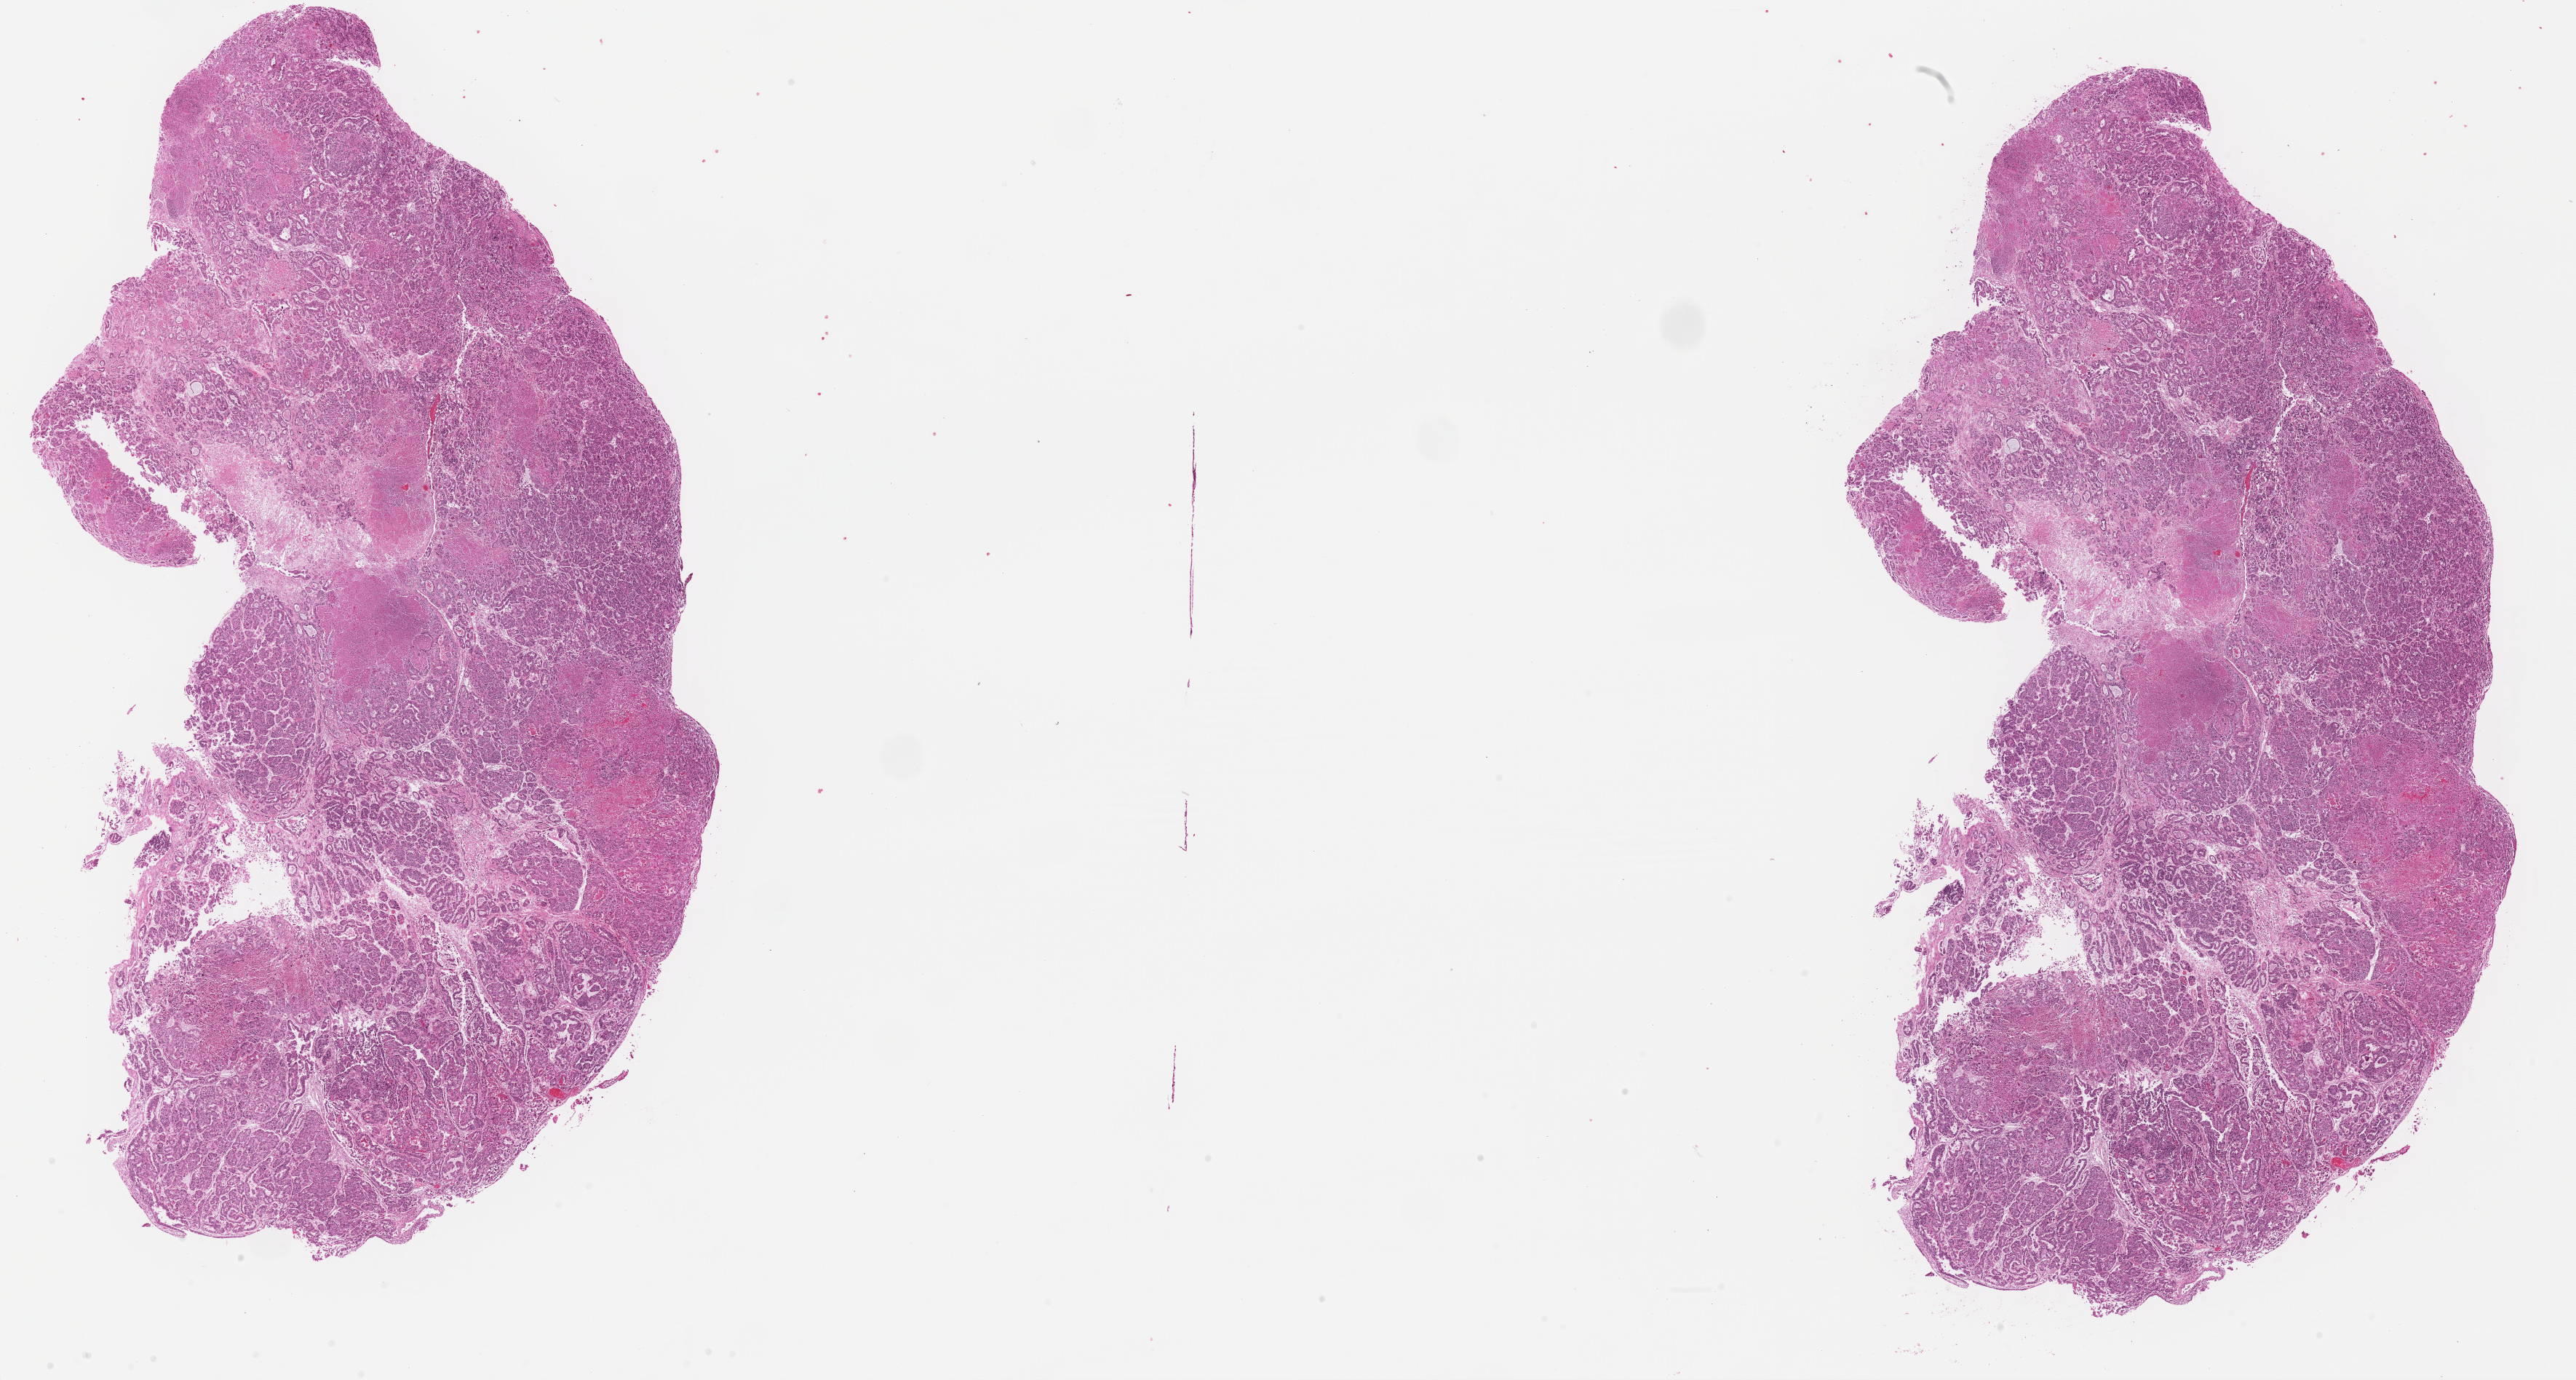
Whole-slide histology image, Hematoxylin and eosin (H&E) stained, low-resolution overview of the scanned area, about 28.0 x 15.0 mm (slide scanned at 40x); formalin-fixed paraffin-embedded (FFPE) diagnostic section; uterus, primary tumour sample. Female patient; age at initial diagnosis 75 years. Histologic grade: G3 (poorly differentiated).
* diagnosis: Serous cystadenocarcinoma, NOS (endometrium)
* lymph nodes positive (case pathology): 0 of 11 examined
* FIGO stage: IIIC1